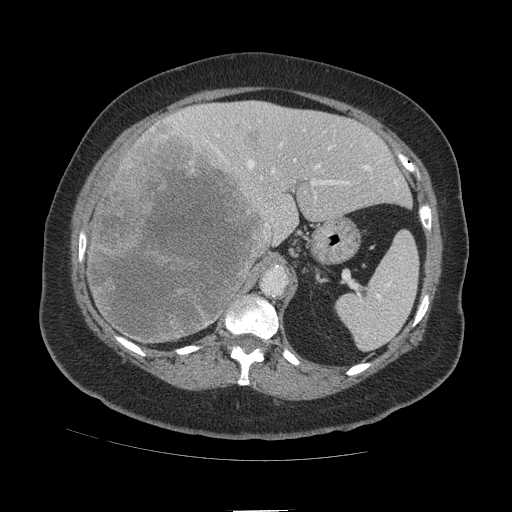
Contrast-enhanced abdominal CT (liver protocol), one axial slice. Position 71 of 109 along the scan axis. Reconstruction kernel STANDARD. Soft-tissue window (W 400 / L 40 HU). 512 × 512 image matrix, field of view 420 × 420 mm. From the clinical record (not read from this slice): diagnosis: hepatocellular carcinoma (patient treated with transarterial chemoembolisation; whether this scan precedes or follows treatment is not stated here); TNM stage (as recorded): Stage-IVB; Child-Pugh class: A; tumour differentiation: poorly differentiated.
Outlined on this slice (semi-automatic segmentation, software-assisted and operator-edited):
- liver parenchyma outside the tumour (the mass and vessels are separate outlines, so this box may not span the whole liver): box from (x=88, y=100) to (x=410, y=340) px
- mass: (x=89, y=121)–(x=270, y=347)
- liver vessels: (x=173, y=113)–(x=398, y=199)